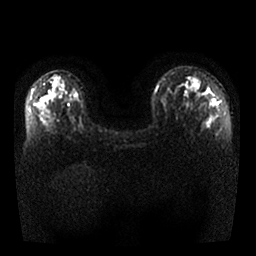
Breast MRI, one axial slice. Slice 16 of 25 in the series (ordered by position). Diffusion-weighted series; image 2 of 4 stored at this slice position (different b-values; order by instance number). 1.5 T. 4 mm slice thickness. 256 × 256 image matrix, field of view 340 × 340 mm. Female patient.
Outlined on this slice (expert manual segmentation):
- tumour on diffusion-weighted imaging: bounding box <186,73,220,105> (left, top, right, bottom; pixels)